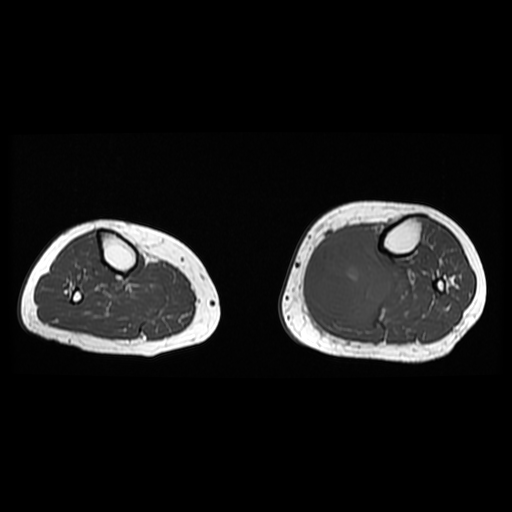
MRI of an extremity soft-tissue mass, one axial slice; slice 16 of 38 in the series (ordered by position); 6 mm slice thickness; 512 × 512 image matrix, field of view 330 × 330 mm. Female patient. From the clinical record (not read from this slice): histological type: extraskeletal high grade osteogenic sarcoma; grade: high; site of the primary tumour: left calf.
Structures marked on this image (manually delineated by an expert):
- gross tumour volume (mass): bounding box <308,228,392,325> (left, top, right, bottom; pixels)